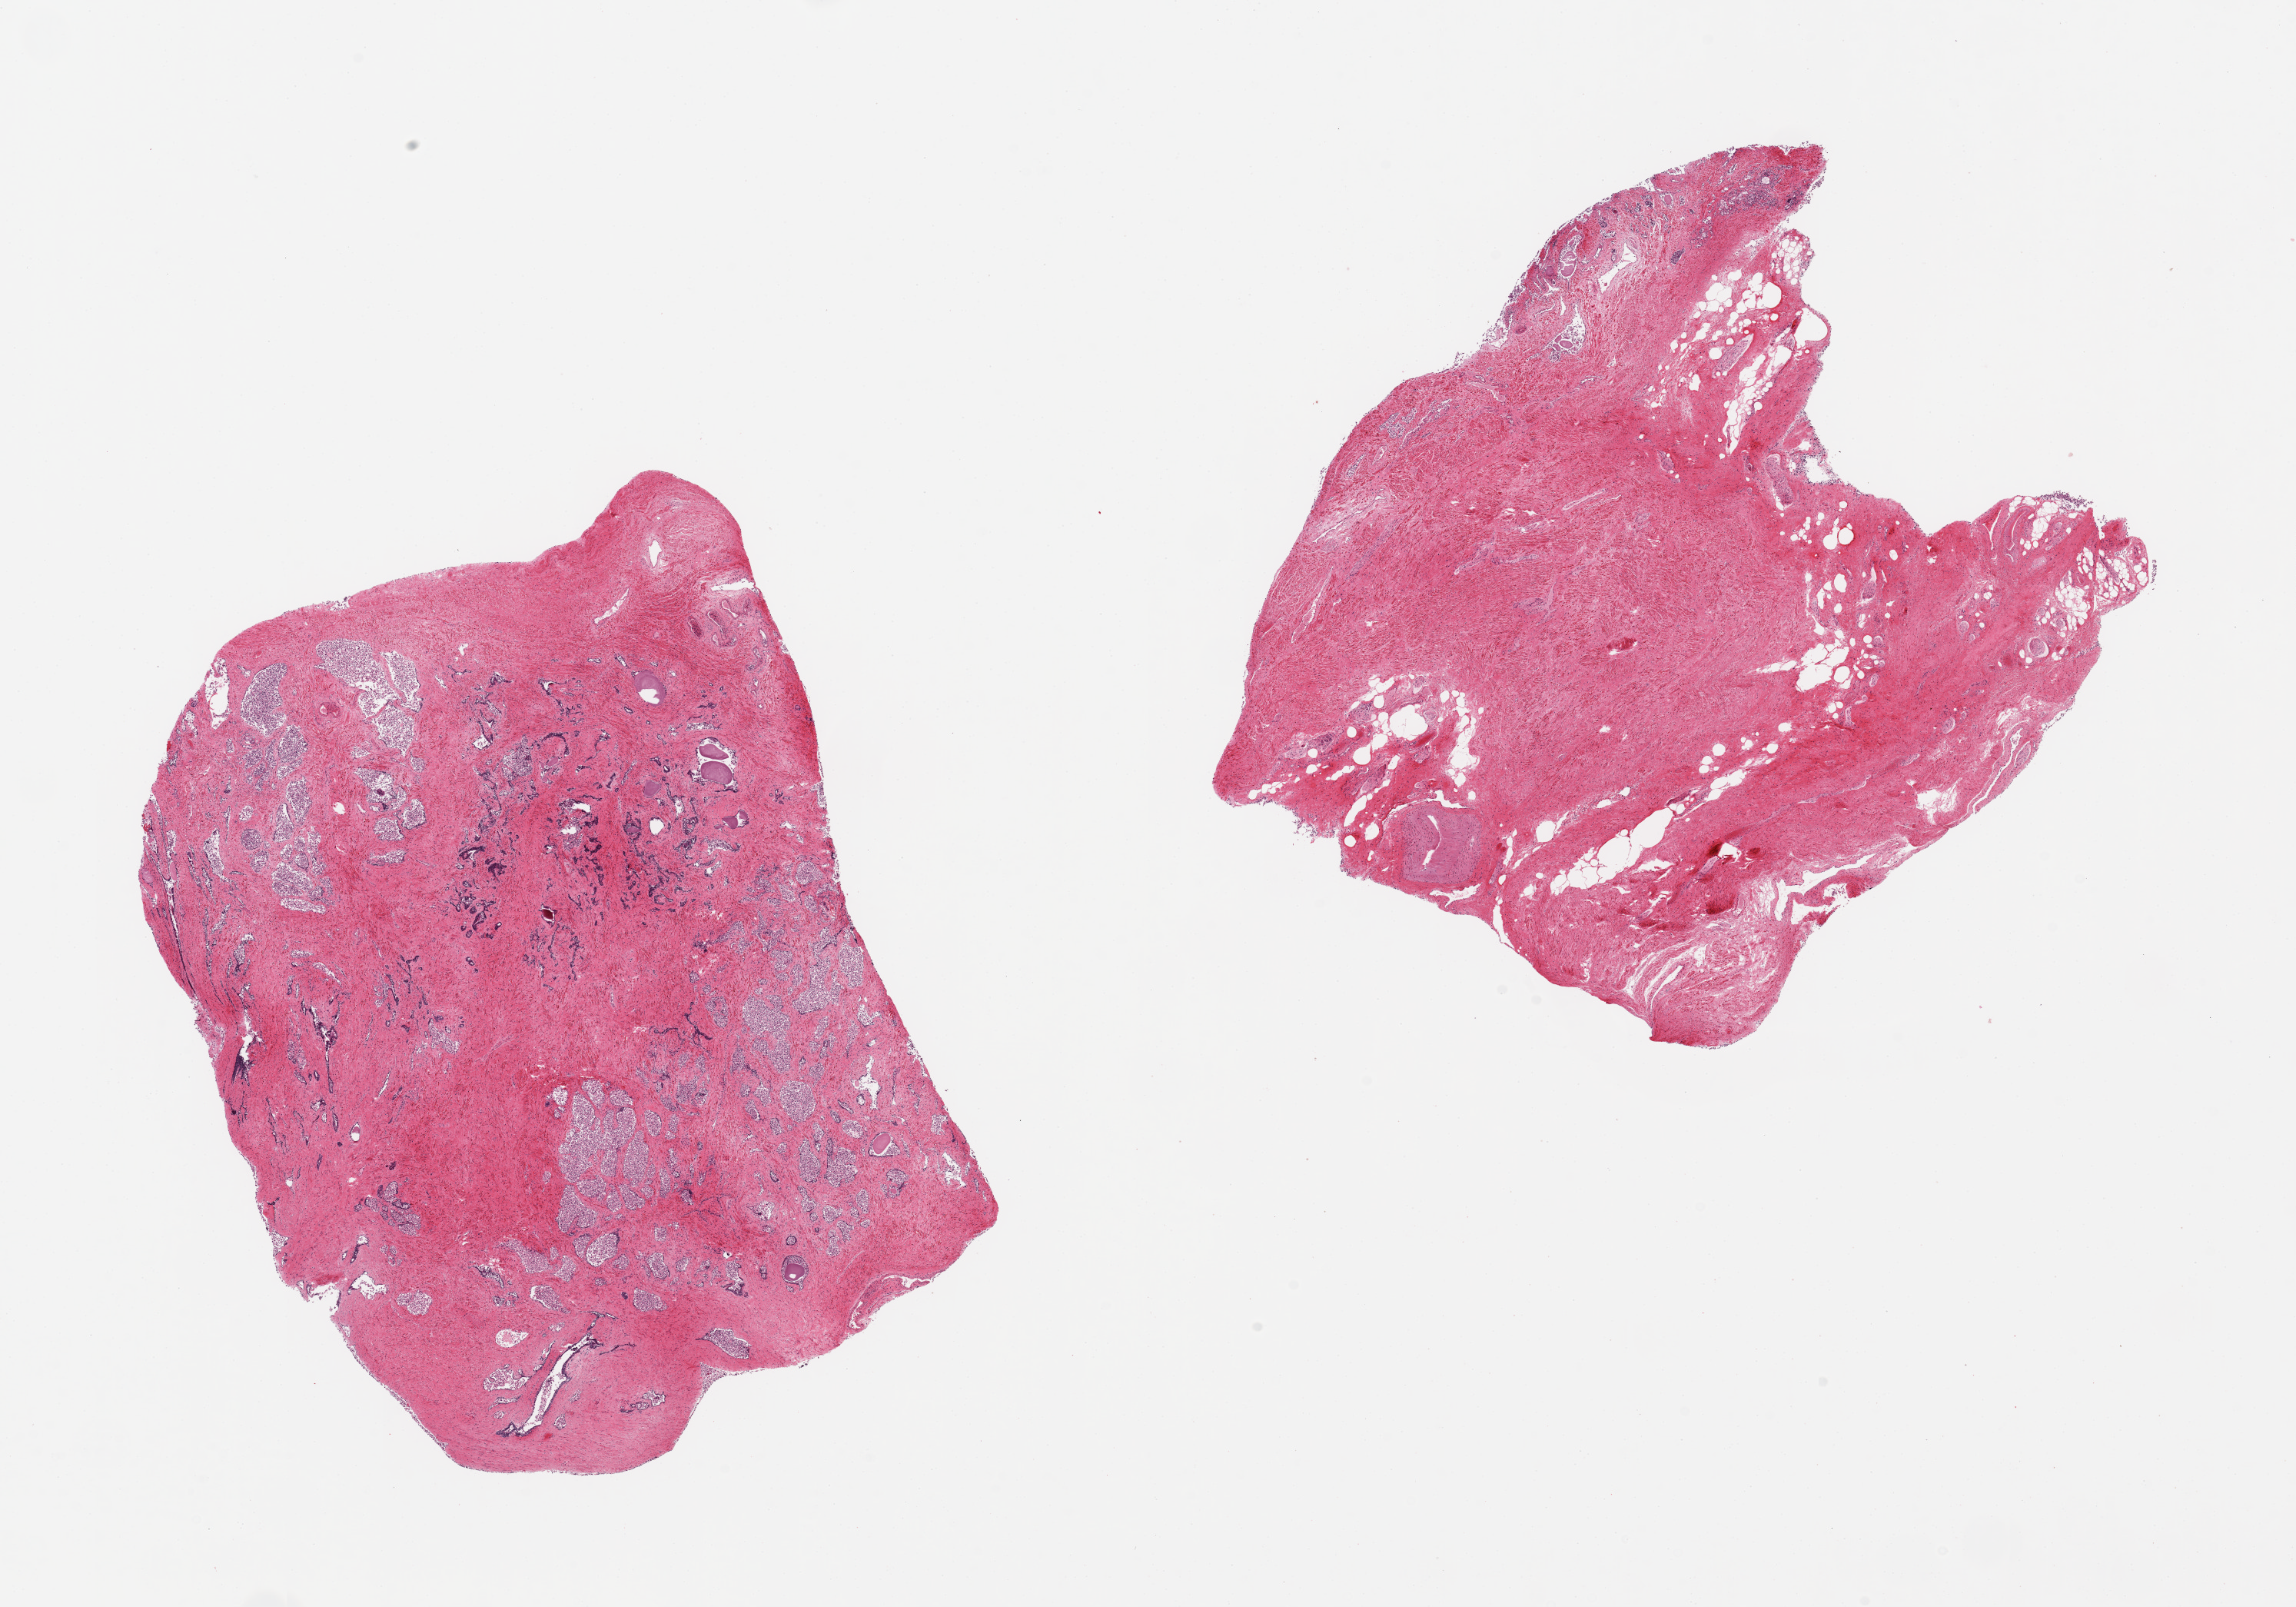
Digitized H&E-stained section — shown as a low-resolution overview of the whole scanned area (about 23.6 x 16.5 mm, acquisition: 20x scan); PAXgene-fixed paraffin-embedded (PFPE) section; section of prostate (target tissue); donor tissue sample. Donor sex: male.
Reviewer comment on this tissue sample: 2 aliquots, ~9x7mm. Glandular component with near-total autolysis.